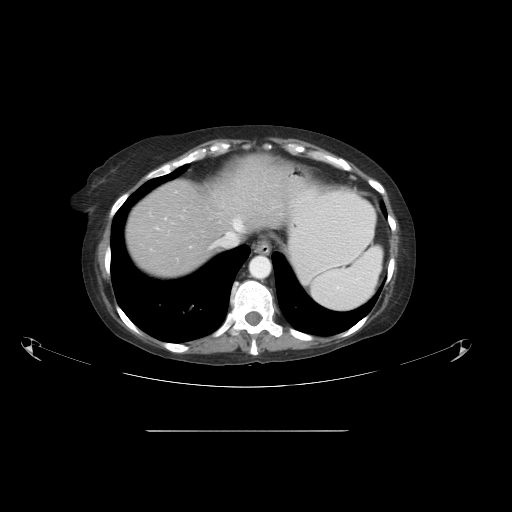
Contrast-enhanced abdominal CT, one axial slice. Slice 43 of 51 in the series (ordered by position). 120 kVp. Intravenous contrast given. Soft-tissue window (W 400 / L 40 HU). 5 mm slice thickness. 512 × 512 image matrix. Female patient, age 48 years. Case-level facts recorded for this patient, not image findings: diagnosis: colorectal cancer liver metastases, imaged before liver resection; multiple liver metastases: yes; largest metastasis: 1 cm; disease in both lobes: no.
Structures marked on this image (outlined manually by an expert reader):
- hepatic veins: box from (x=217, y=219) to (x=243, y=244) px
- liver: (x=126, y=157)–(x=289, y=279)
- planned liver remnant (the part of the liver to remain after resection): (x=126, y=180)–(x=229, y=279)
- portal vein (with intrahepatic branches): (x=158, y=218)–(x=166, y=229)